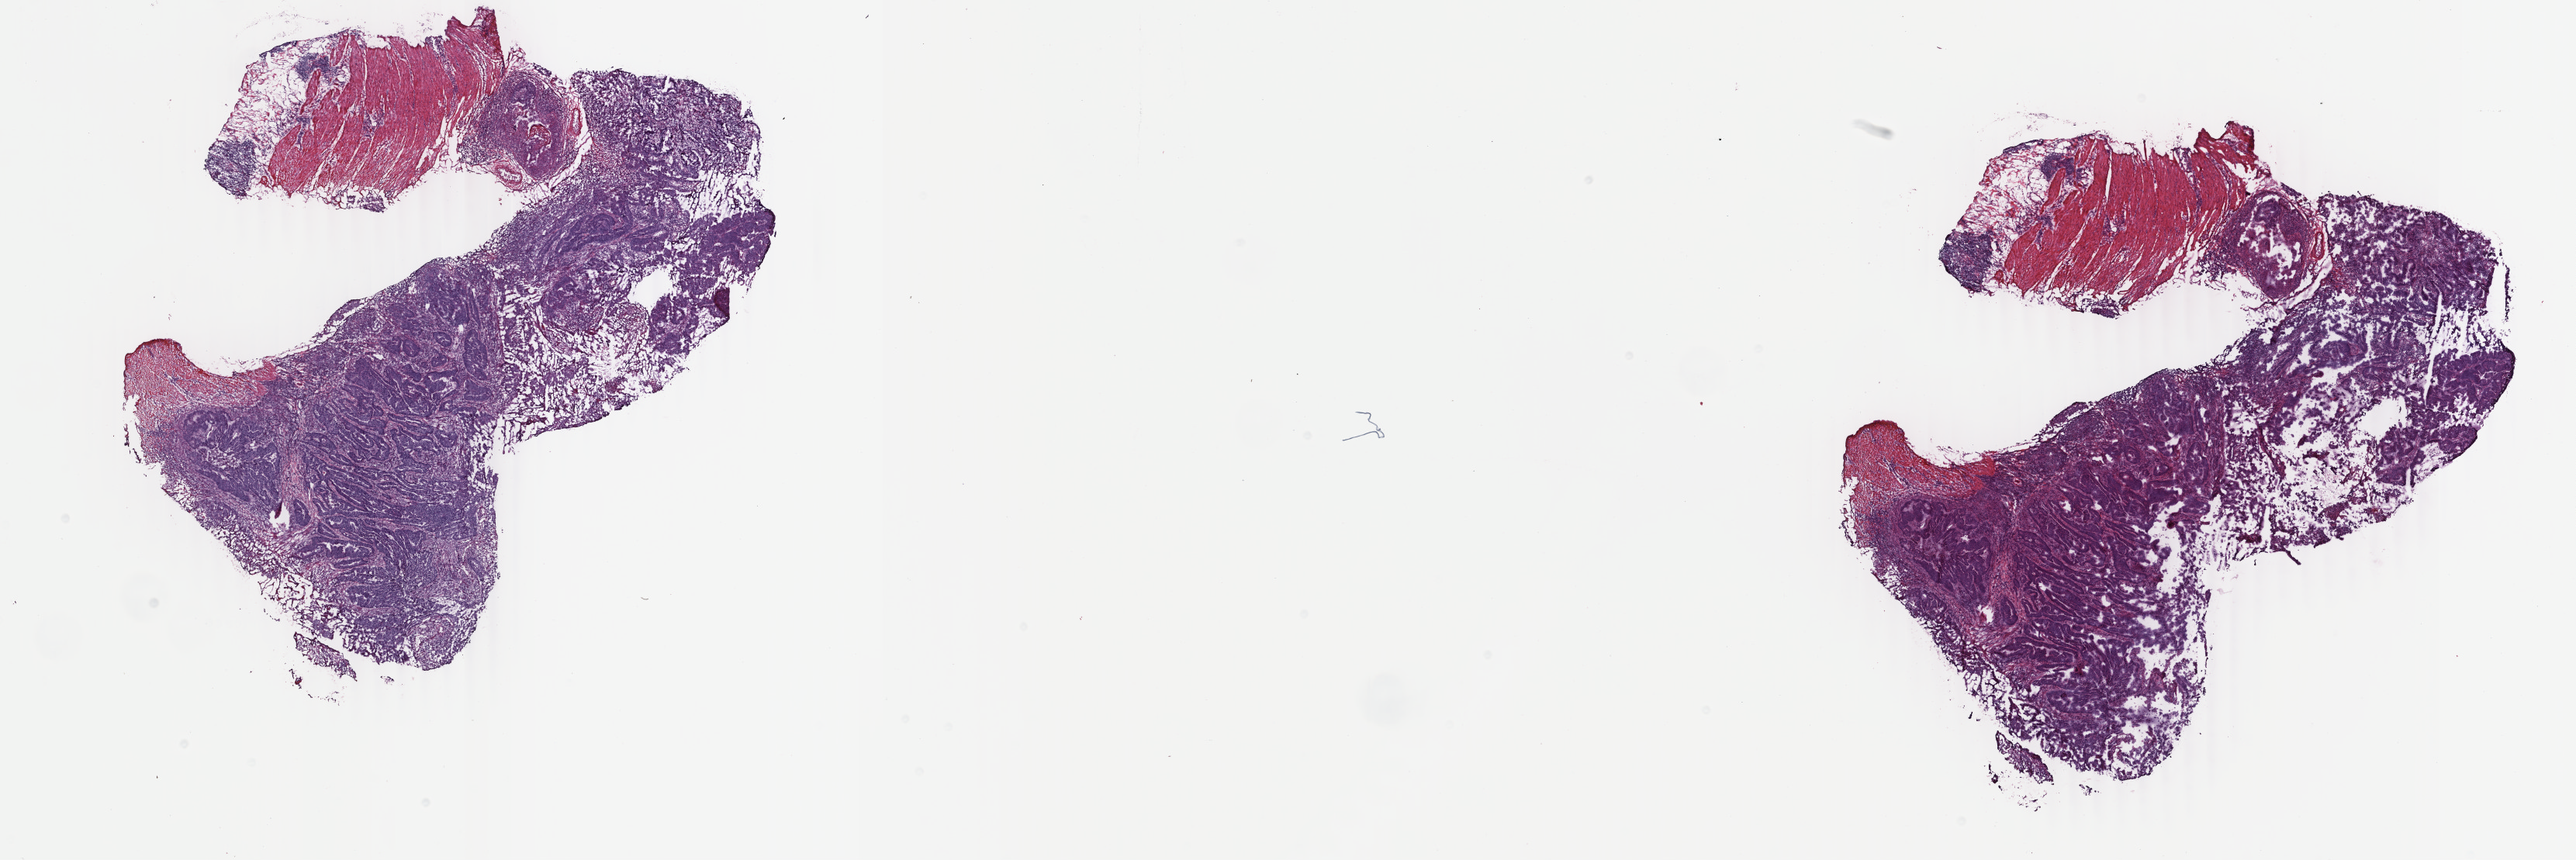
Whole-slide histology image, Hematoxylin and eosin (H&E) stained, low-resolution overview of the scanned area, about 26.4 x 8.8 mm (slide scanned at 40x); frozen section; rectum, primary tumour sample. Patient: female, age at initial diagnosis 49 years. Slide review estimates, as recorded: tumour cells 80%, tumour nuclei 80%, normal cells 0%, stromal cells 18%, necrosis 2%. Inflammatory infiltration, as recorded: lymphocyte infiltration 5%, monocyte infiltration 0%, neutrophil infiltration 0%.
Diagnosis: Adenocarcinoma, NOS. Lymph nodes positive (case pathology): 0 of 17 examined. AJCC pathologic stage: II (5th edition).